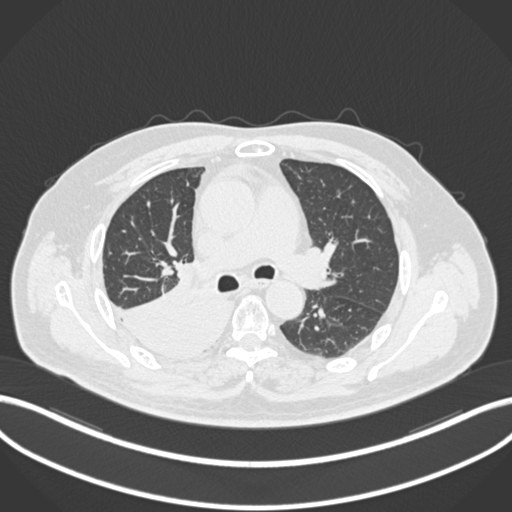
Chest CT, one axial slice; slice 121 of 218 in the series (ordered by position); reconstruction kernel B30f; lung window (W 1500 / L -600 HU); 512 × 512 image matrix, field of view 400 × 400 mm. Male patient, age 68 years. From the clinical record (not read from this slice): clinical TNM (as recorded): T2a N0 M0.
Annotated regions visible in this slice (rectangle marked by the reading radiologist):
- lung tumour (recorded histology: adenocarcinoma): bounding box [x1, y1, x2, y2] px = [109, 285, 232, 360]